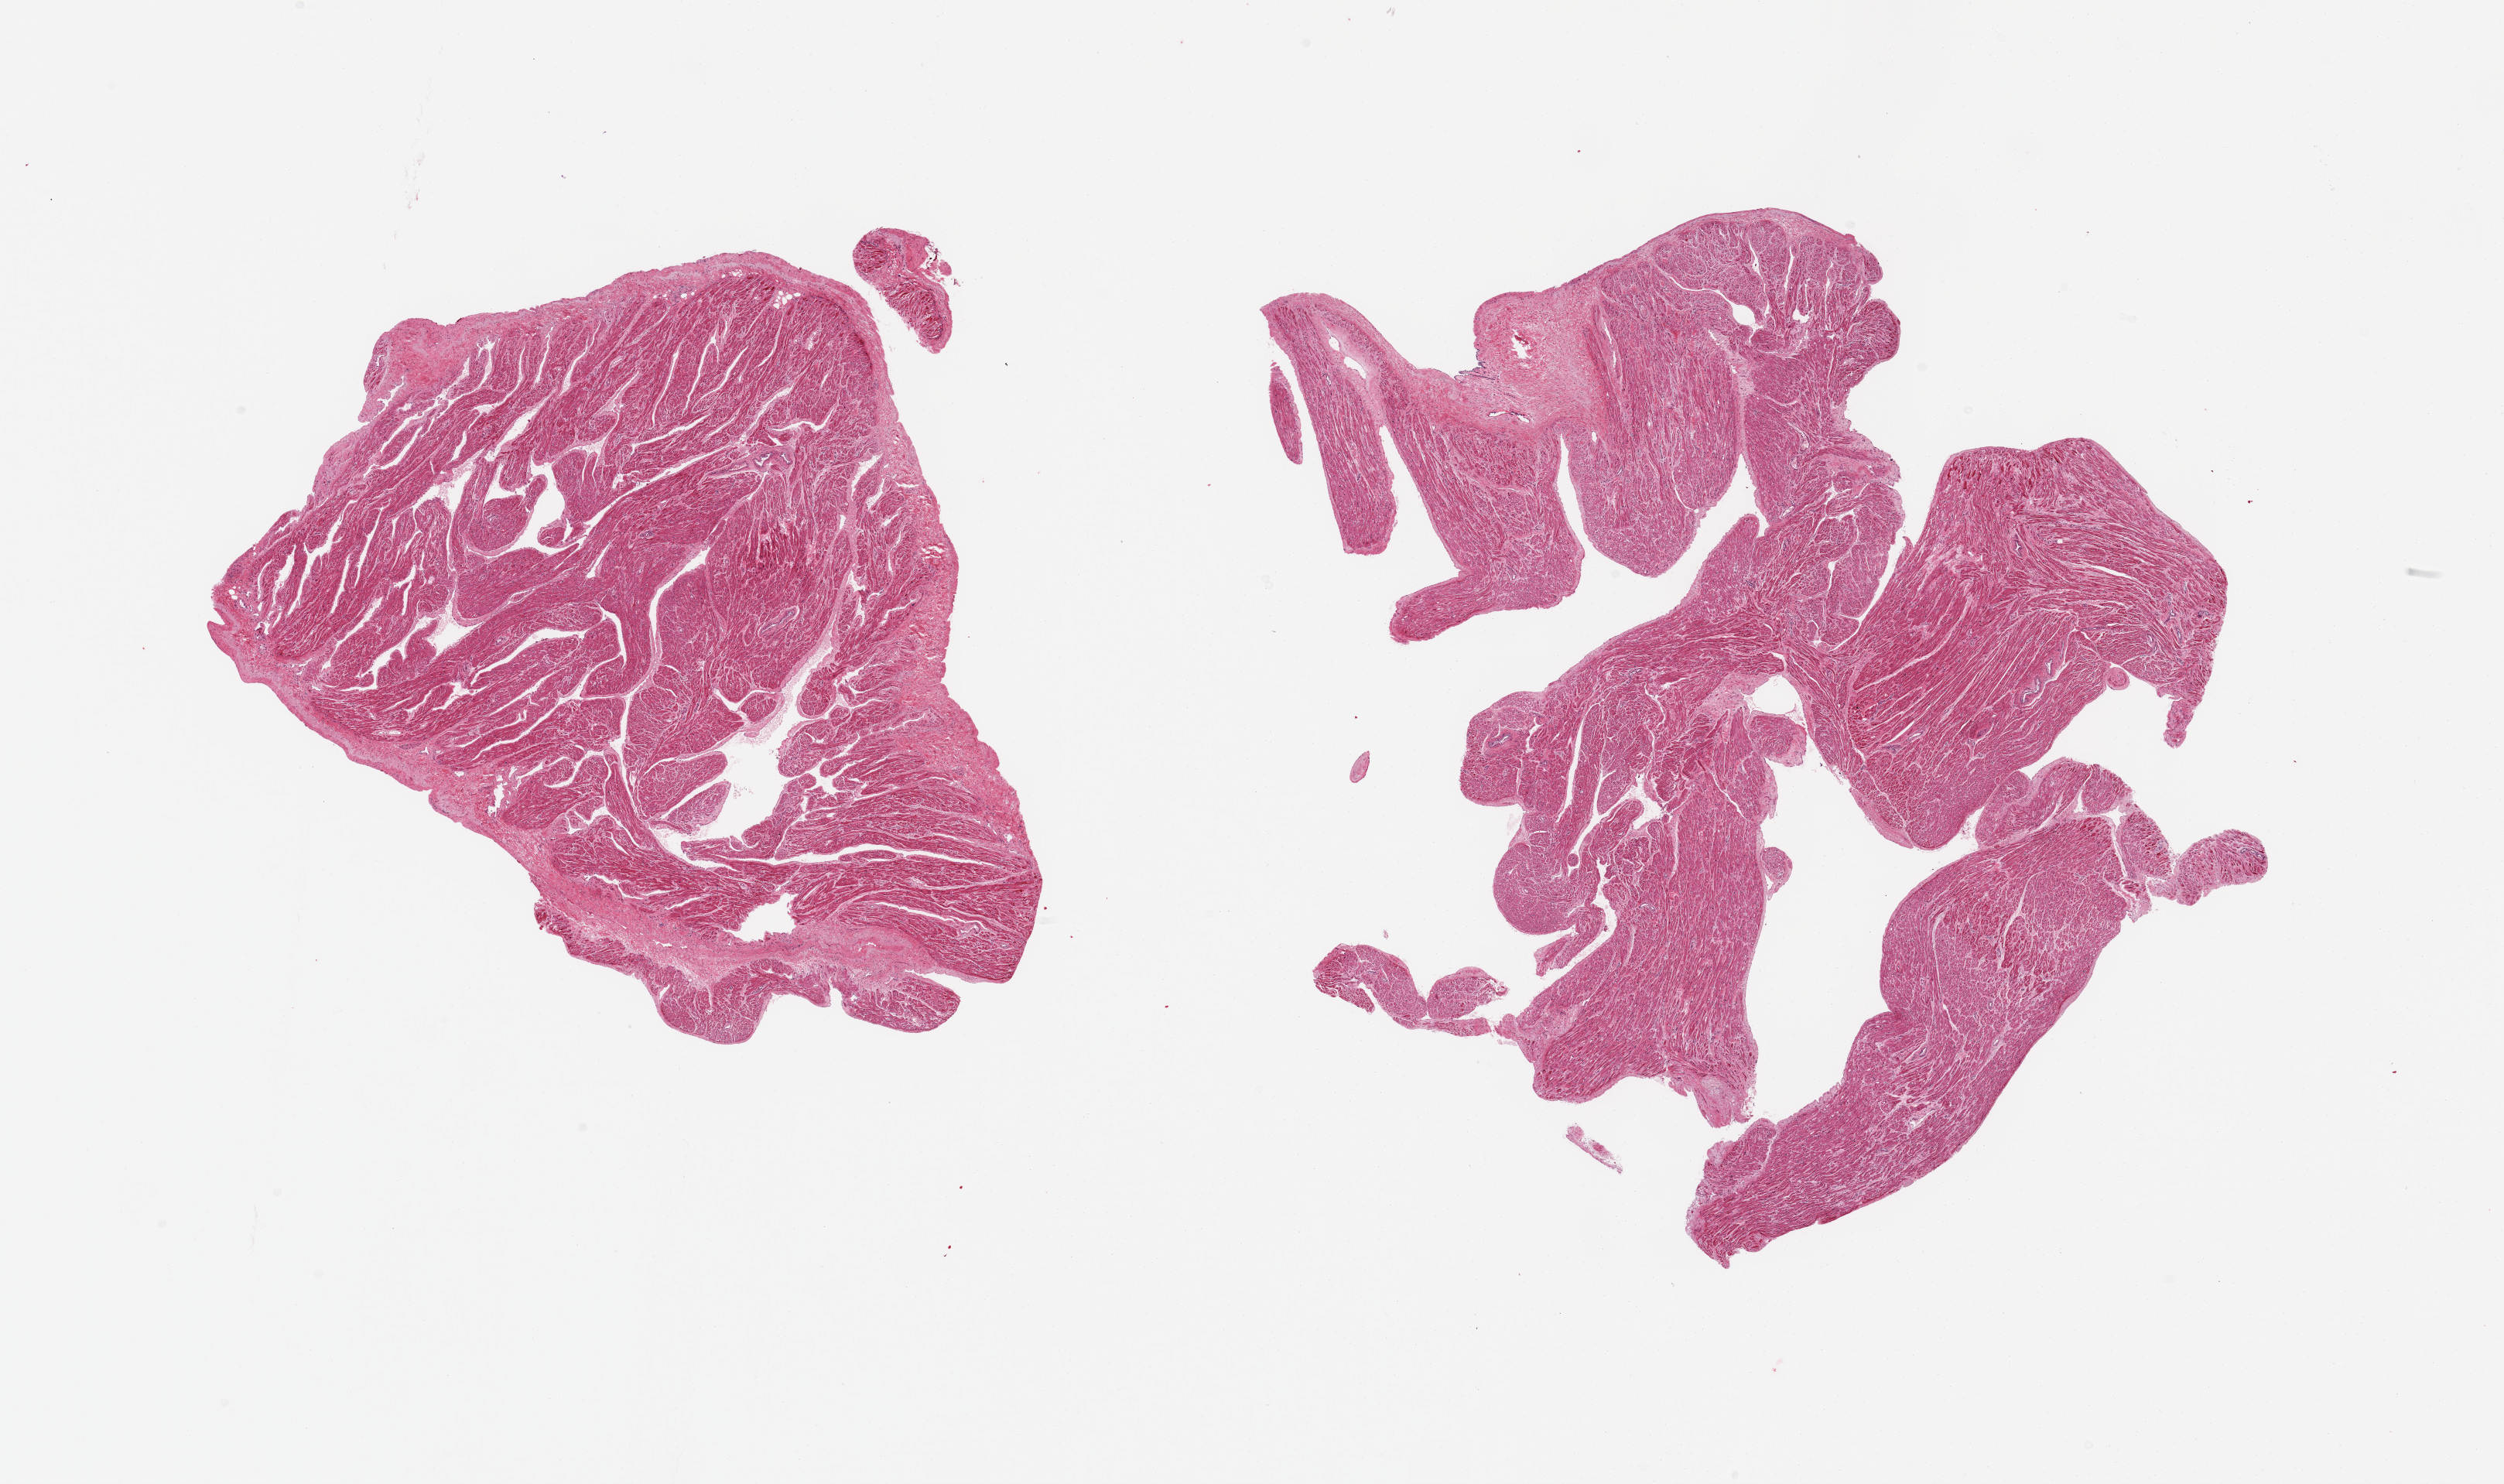
H&E whole-slide image — whole scanned area (about 25.6 x 15.2 mm, from a 20x scan) shown as a low-resolution overview. PAXgene-fixed, paraffin-embedded tissue. Sampled site (target tissue): auricular appendage. Donor tissue sample. Donor: male.
- reviewer comment on this tissue sample: 2 pieces, no abnormalities